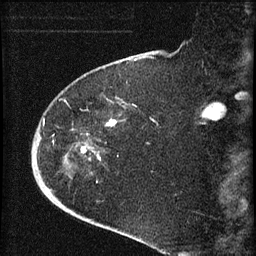
Breast MRI (dynamic contrast-enhanced), one sagittal slice. Dynamic contrast-enhanced series, image 2 of 4 at this slice position (ordered by acquisition). 1.5 T. TE 4.2 ms, TR 8.2 ms. 2 mm slice thickness. 256 × 256 image matrix. Patient: female, 71 years.
Outlined on this slice (semi-automatic segmentation, software-assisted and operator-edited):
- analysis volume of interest (the breast-tissue region the enhancement analysis was run in; not a lesion): bounding box <35,75,129,190> (left, top, right, bottom; pixels)
- tumour enhancement mask (voxels above the 70 % enhancement threshold inside the analysis volume of interest): <82,120,116,159>